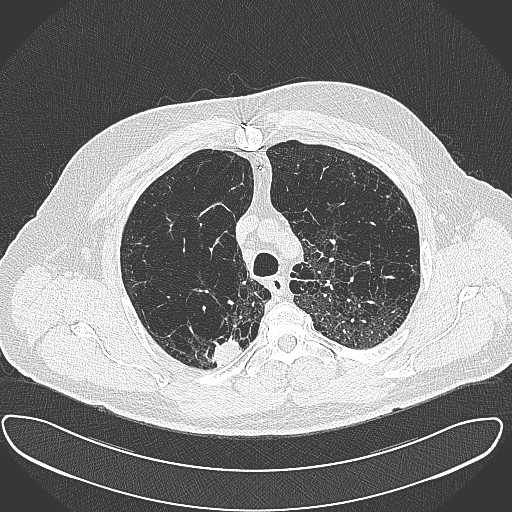
Chest CT (low-dose screening protocol), one axial image. First (baseline) screen. Lung window (W 1500 / L -600 HU). 1 mm slice thickness. 512 × 512 image matrix. Male participant, aged 60 years at enrolment. Current smoker at enrolment.
• Lesion marked by an expert reader, bounding box (x1, y1, x2, y2) in pixels: (199, 327, 243, 367).
• Screening reader's record for this exam (one nodule recorded; not confirmed to be the boxed lesion): non-calcified nodule or mass ≥4 mm, right upper lobe, 15 × 25 mm, spiculated (stellate) margins, soft tissue attenuation.
• Official screen result: positive, change unspecified: nodule(s) >= 4 mm or enlarging nodule(s), mass(es), or other non-specific abnormalities suspicious for lung cancer.
• Participant outcome: lung cancer diagnosed 32 days after this screen — carcinoma, NOS, right upper lobe, moderately differentiated (G2), stage IB (AJCC 6th edition), 35 mm at pathology.